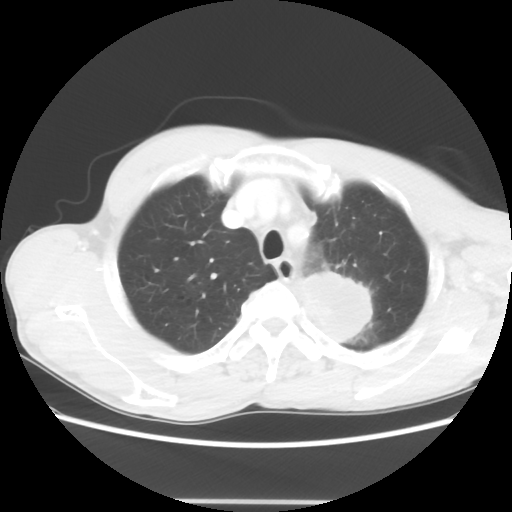
Chest CT, one axial slice. Position 53 of 62 along the scan axis. Reconstruction kernel STANDARD. 100 kVp. Lung window (W 1500 / L -600 HU). 5 mm slice thickness. 512 × 512 image matrix. Male patient, age 61 years. From the clinical record (not read from this slice): clinical TNM (as recorded): T3 N1 M1.
Outlined on this slice (rectangle marked by the reading radiologist):
- lung tumour (recorded histology: adenocarcinoma): box from (x=300, y=265) to (x=379, y=352) px